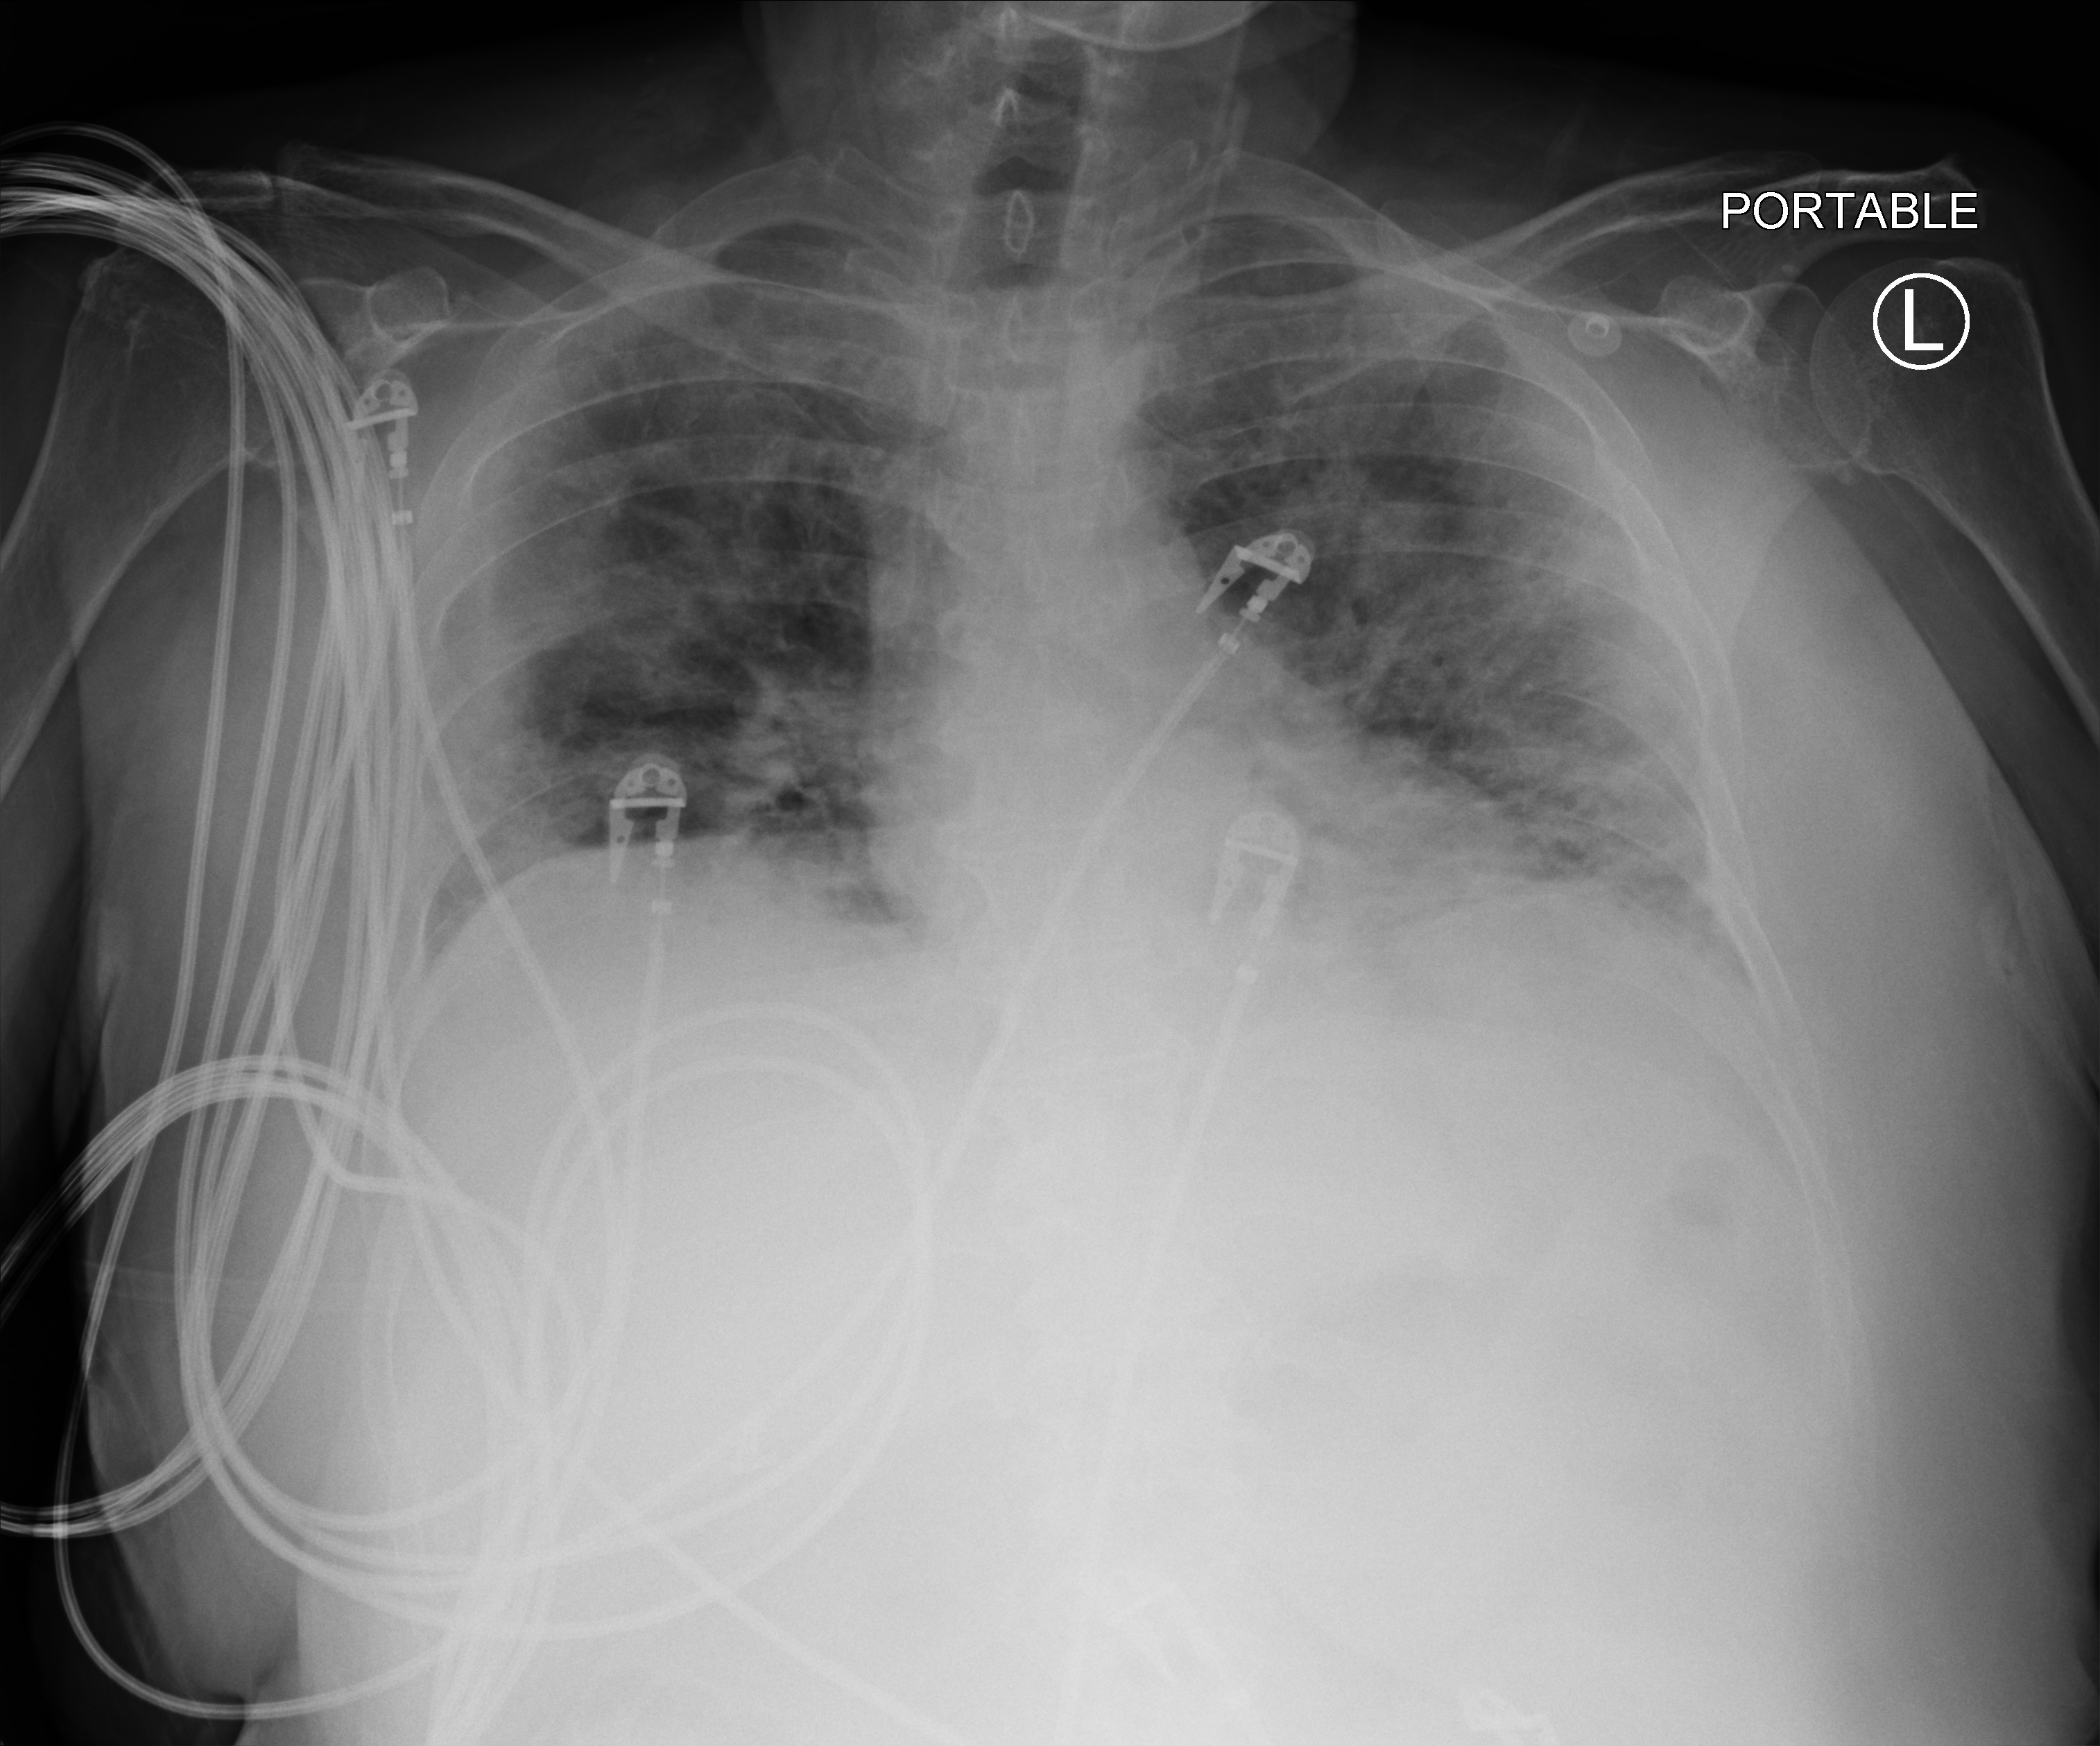
Portable chest radiograph; anteroposterior (AP) projection. Patient hospitalised with COVID-19; female, aged 18–59 years.
Admission-level facts for this patient (not findings on this image; timing relative to this image not recorded): chronic kidney disease (admission record): no; mechanically ventilated during this hospital stay: no.